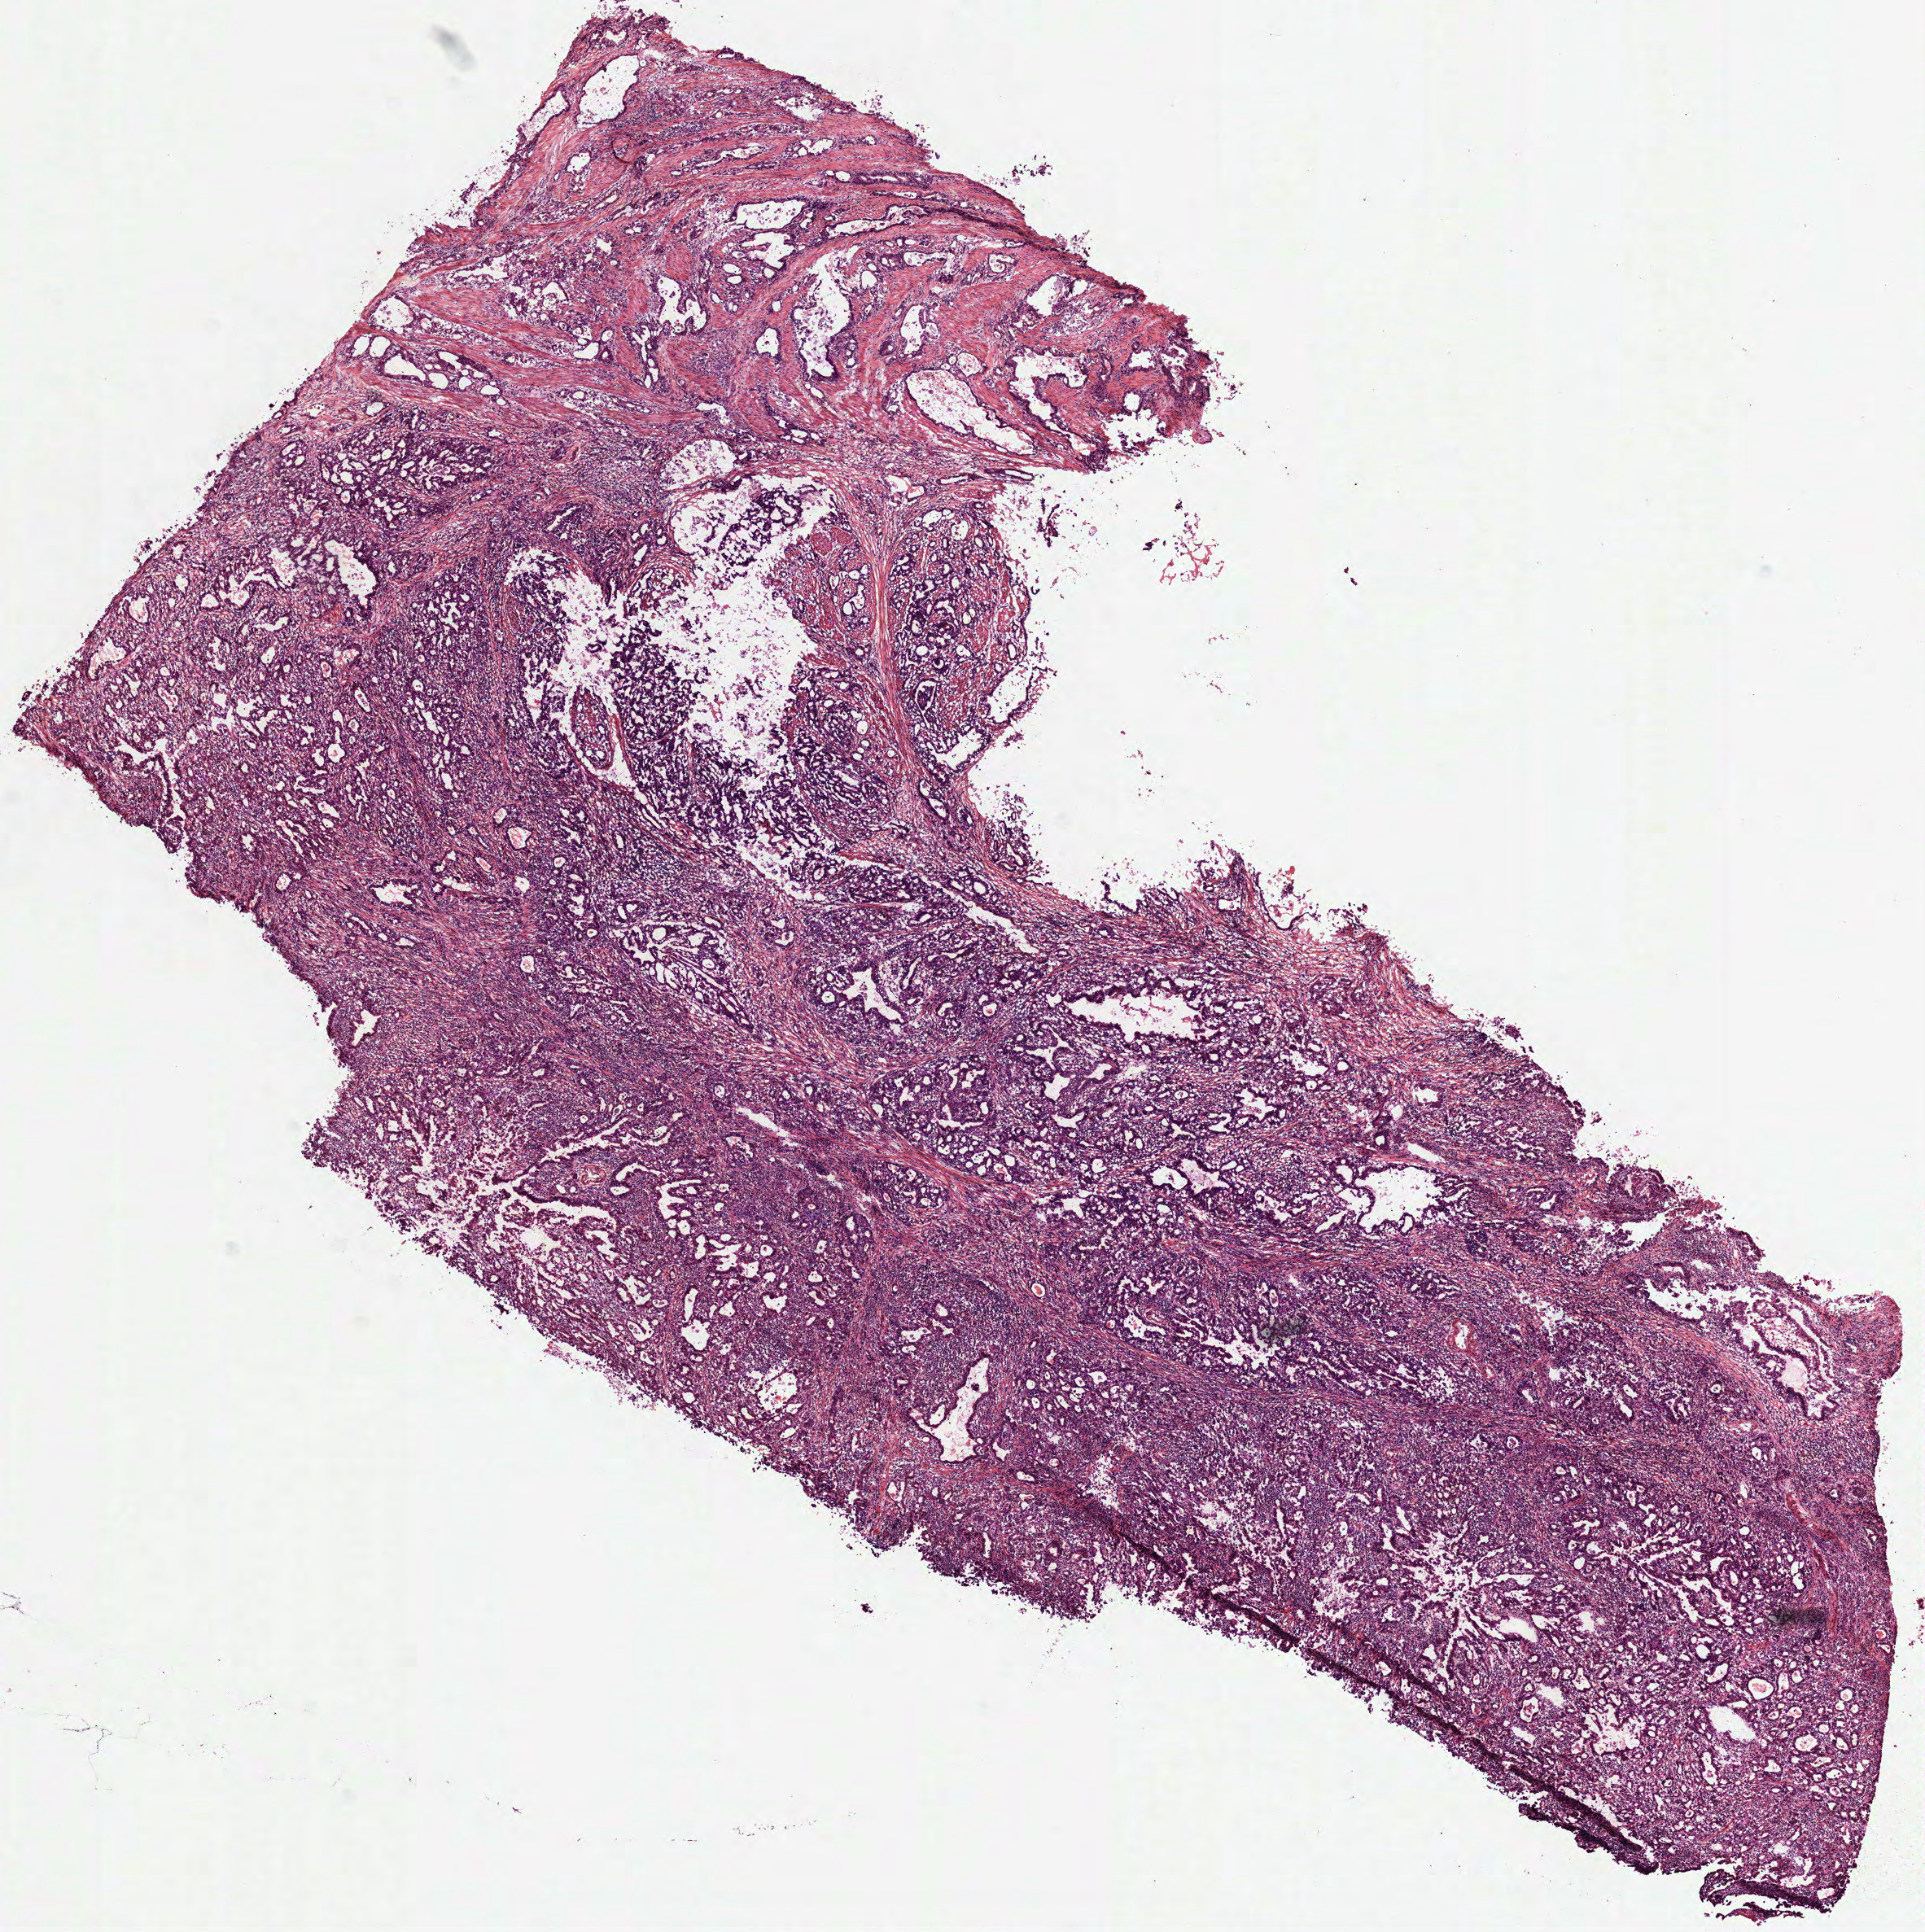
Whole-slide histology image, H&E-stained, whole scanned area (about 9.5 x 9.6 mm, slide scanned at 40x) shown as a low-resolution overview, frozen section from the top of the tissue portion, sample: primary tumour, stomach. Patient: male, age at initial diagnosis 52 years. Histologic grade: G2 (moderately differentiated). Composition of this section per pathologist review: tumour cells 85%, tumour nuclei 60%, normal cells 0%, stromal cells 15%, necrosis 0%.
AJCC pathologic stage: II (6th edition). Diagnosis: Adenocarcinoma, NOS (cardia, NOS).